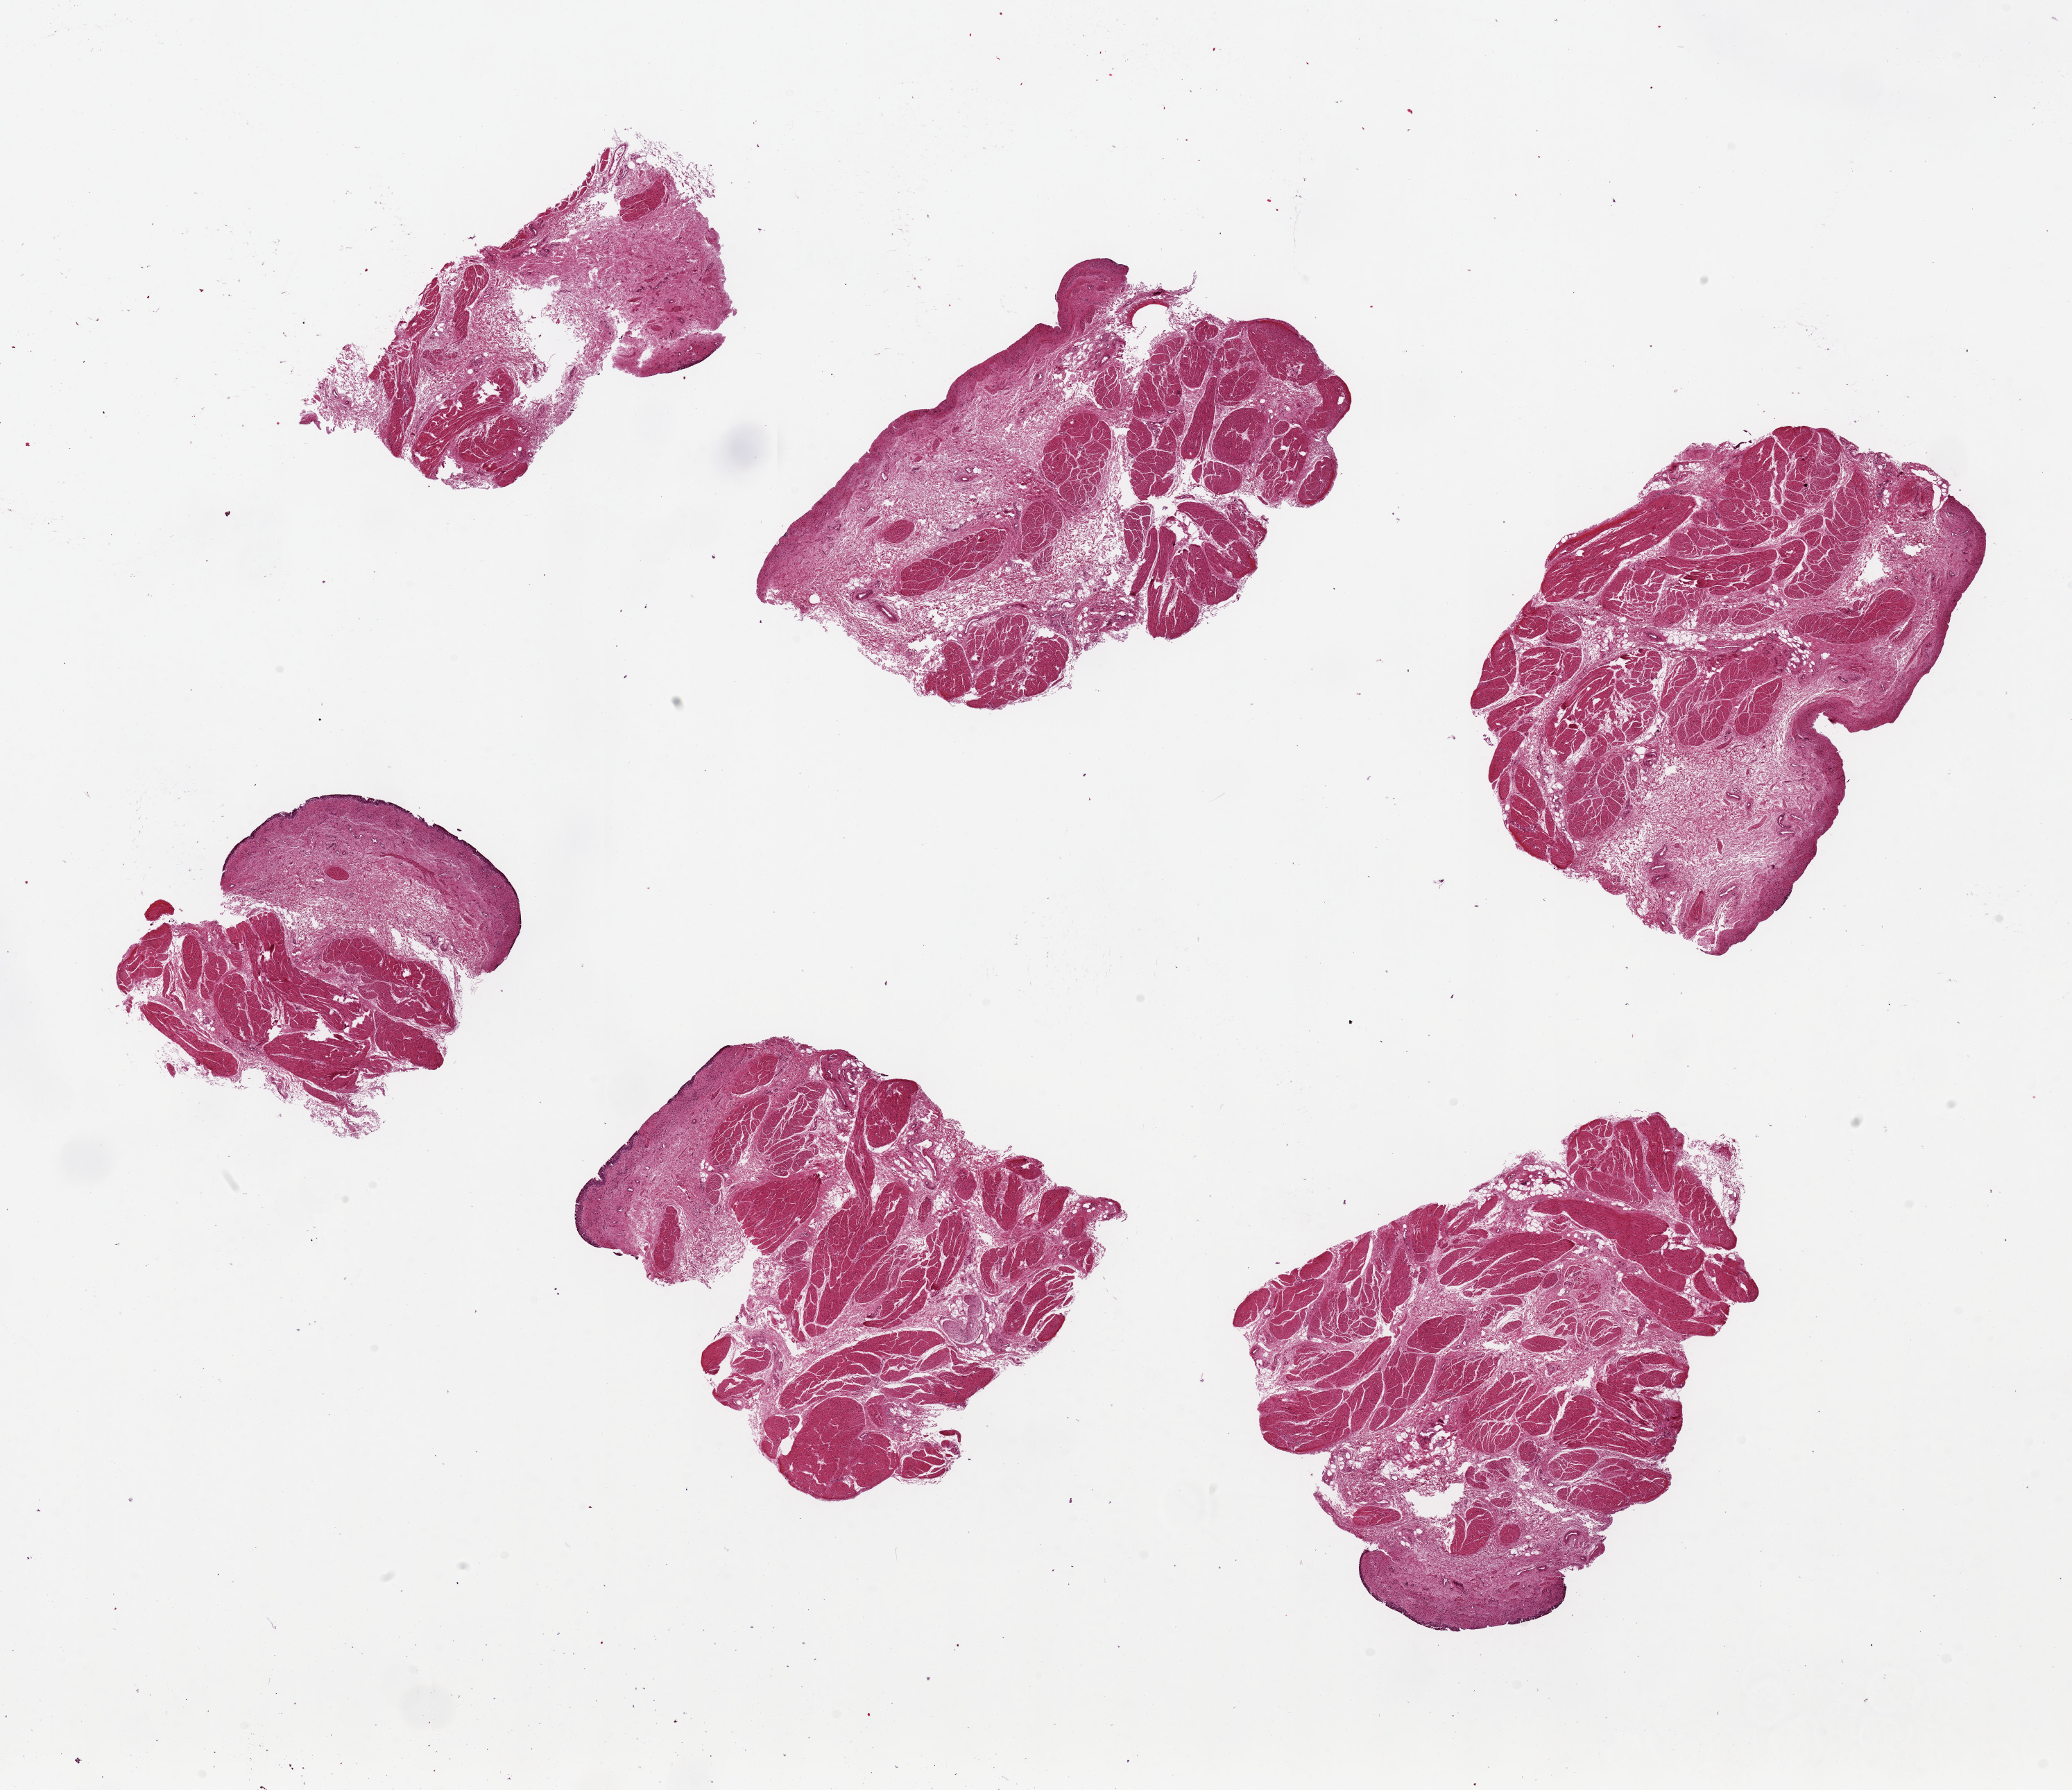
Digitized haematoxylin and eosin-stained section, brightfield, low-resolution overview of the scanned area, about 23.6 x 20.4 mm, PAXgene-fixed paraffin-embedded (PFPE) section, sampled site (target tissue): urinary bladder, tissue donor sample. Donor sex: female.
- reviewer comment on this tissue sample: 6 pieces mucosa, ~ 6x3mm sloughed mucosa: not vagina but additional bladder. May be used as such when relabled